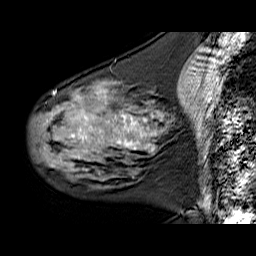
Breast MRI (dynamic contrast-enhanced), one sagittal slice. Slice 23 of 60 in the series (ordered by position). Dynamic contrast-enhanced series, time point 2 of 6 at this slice position (early post-contrast). 1.5 T. TE 6.3 ms, TR 32.9 ms. 256 × 256 image matrix. Female patient. Case-level facts recorded for this patient, not image findings: setting: breast cancer imaged before/during neoadjuvant chemotherapy; receptor status: HER2-positive.
Outlined on this slice (semi-automatic segmentation, software-assisted and operator-edited):
- analysis volume of interest (the breast-tissue region the enhancement analysis was run in; not a lesion): bounding box [x1, y1, x2, y2] px = [32, 80, 170, 180]
- tumour enhancement mask (voxels above the 100 % enhancement threshold inside the analysis volume of interest): [72, 94, 157, 151]